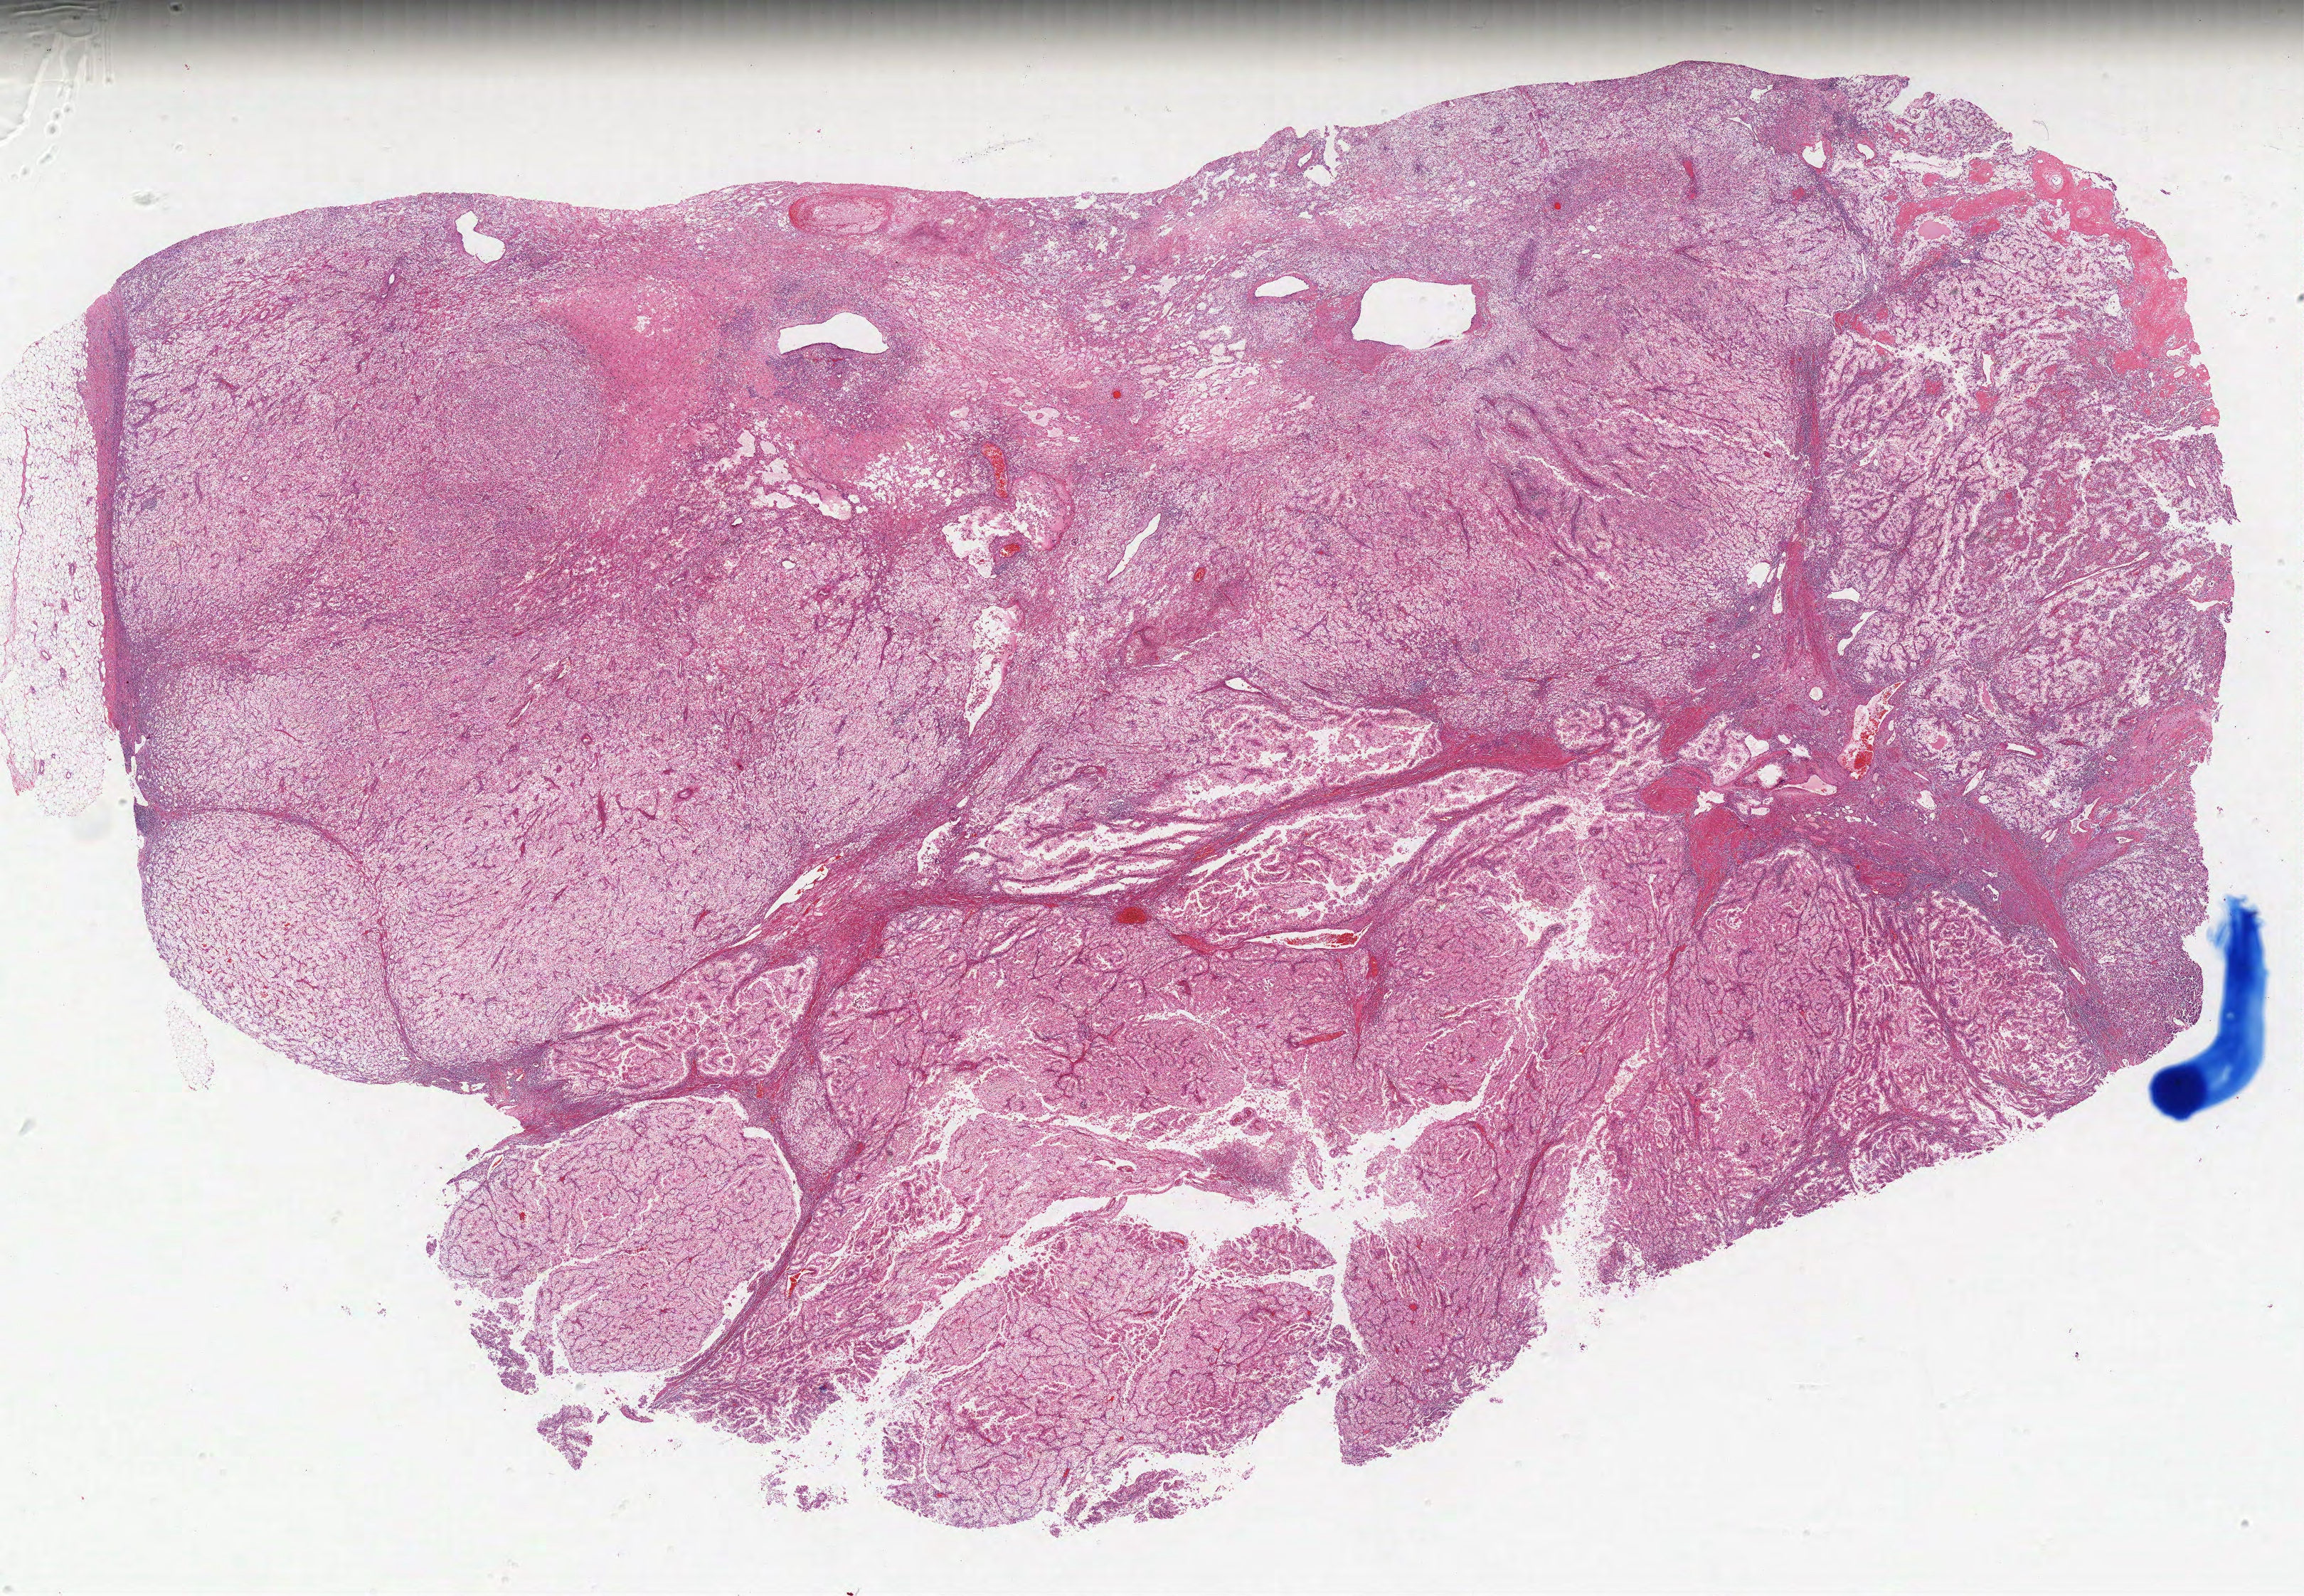
H&E-stained whole-slide image, whole scanned area (about 25.9 x 17.9 mm, from a 40x scan) shown as a low-resolution overview. Formalin-fixed paraffin-embedded (FFPE) diagnostic section. Sample: primary tumour, kidney. Male patient; age at initial diagnosis 74 years. Histologic grade: G4 (undifferentiated).
Diagnosis: Clear cell adenocarcinoma, NOS. Lymph nodes positive (case pathology): 0 of 30 examined.